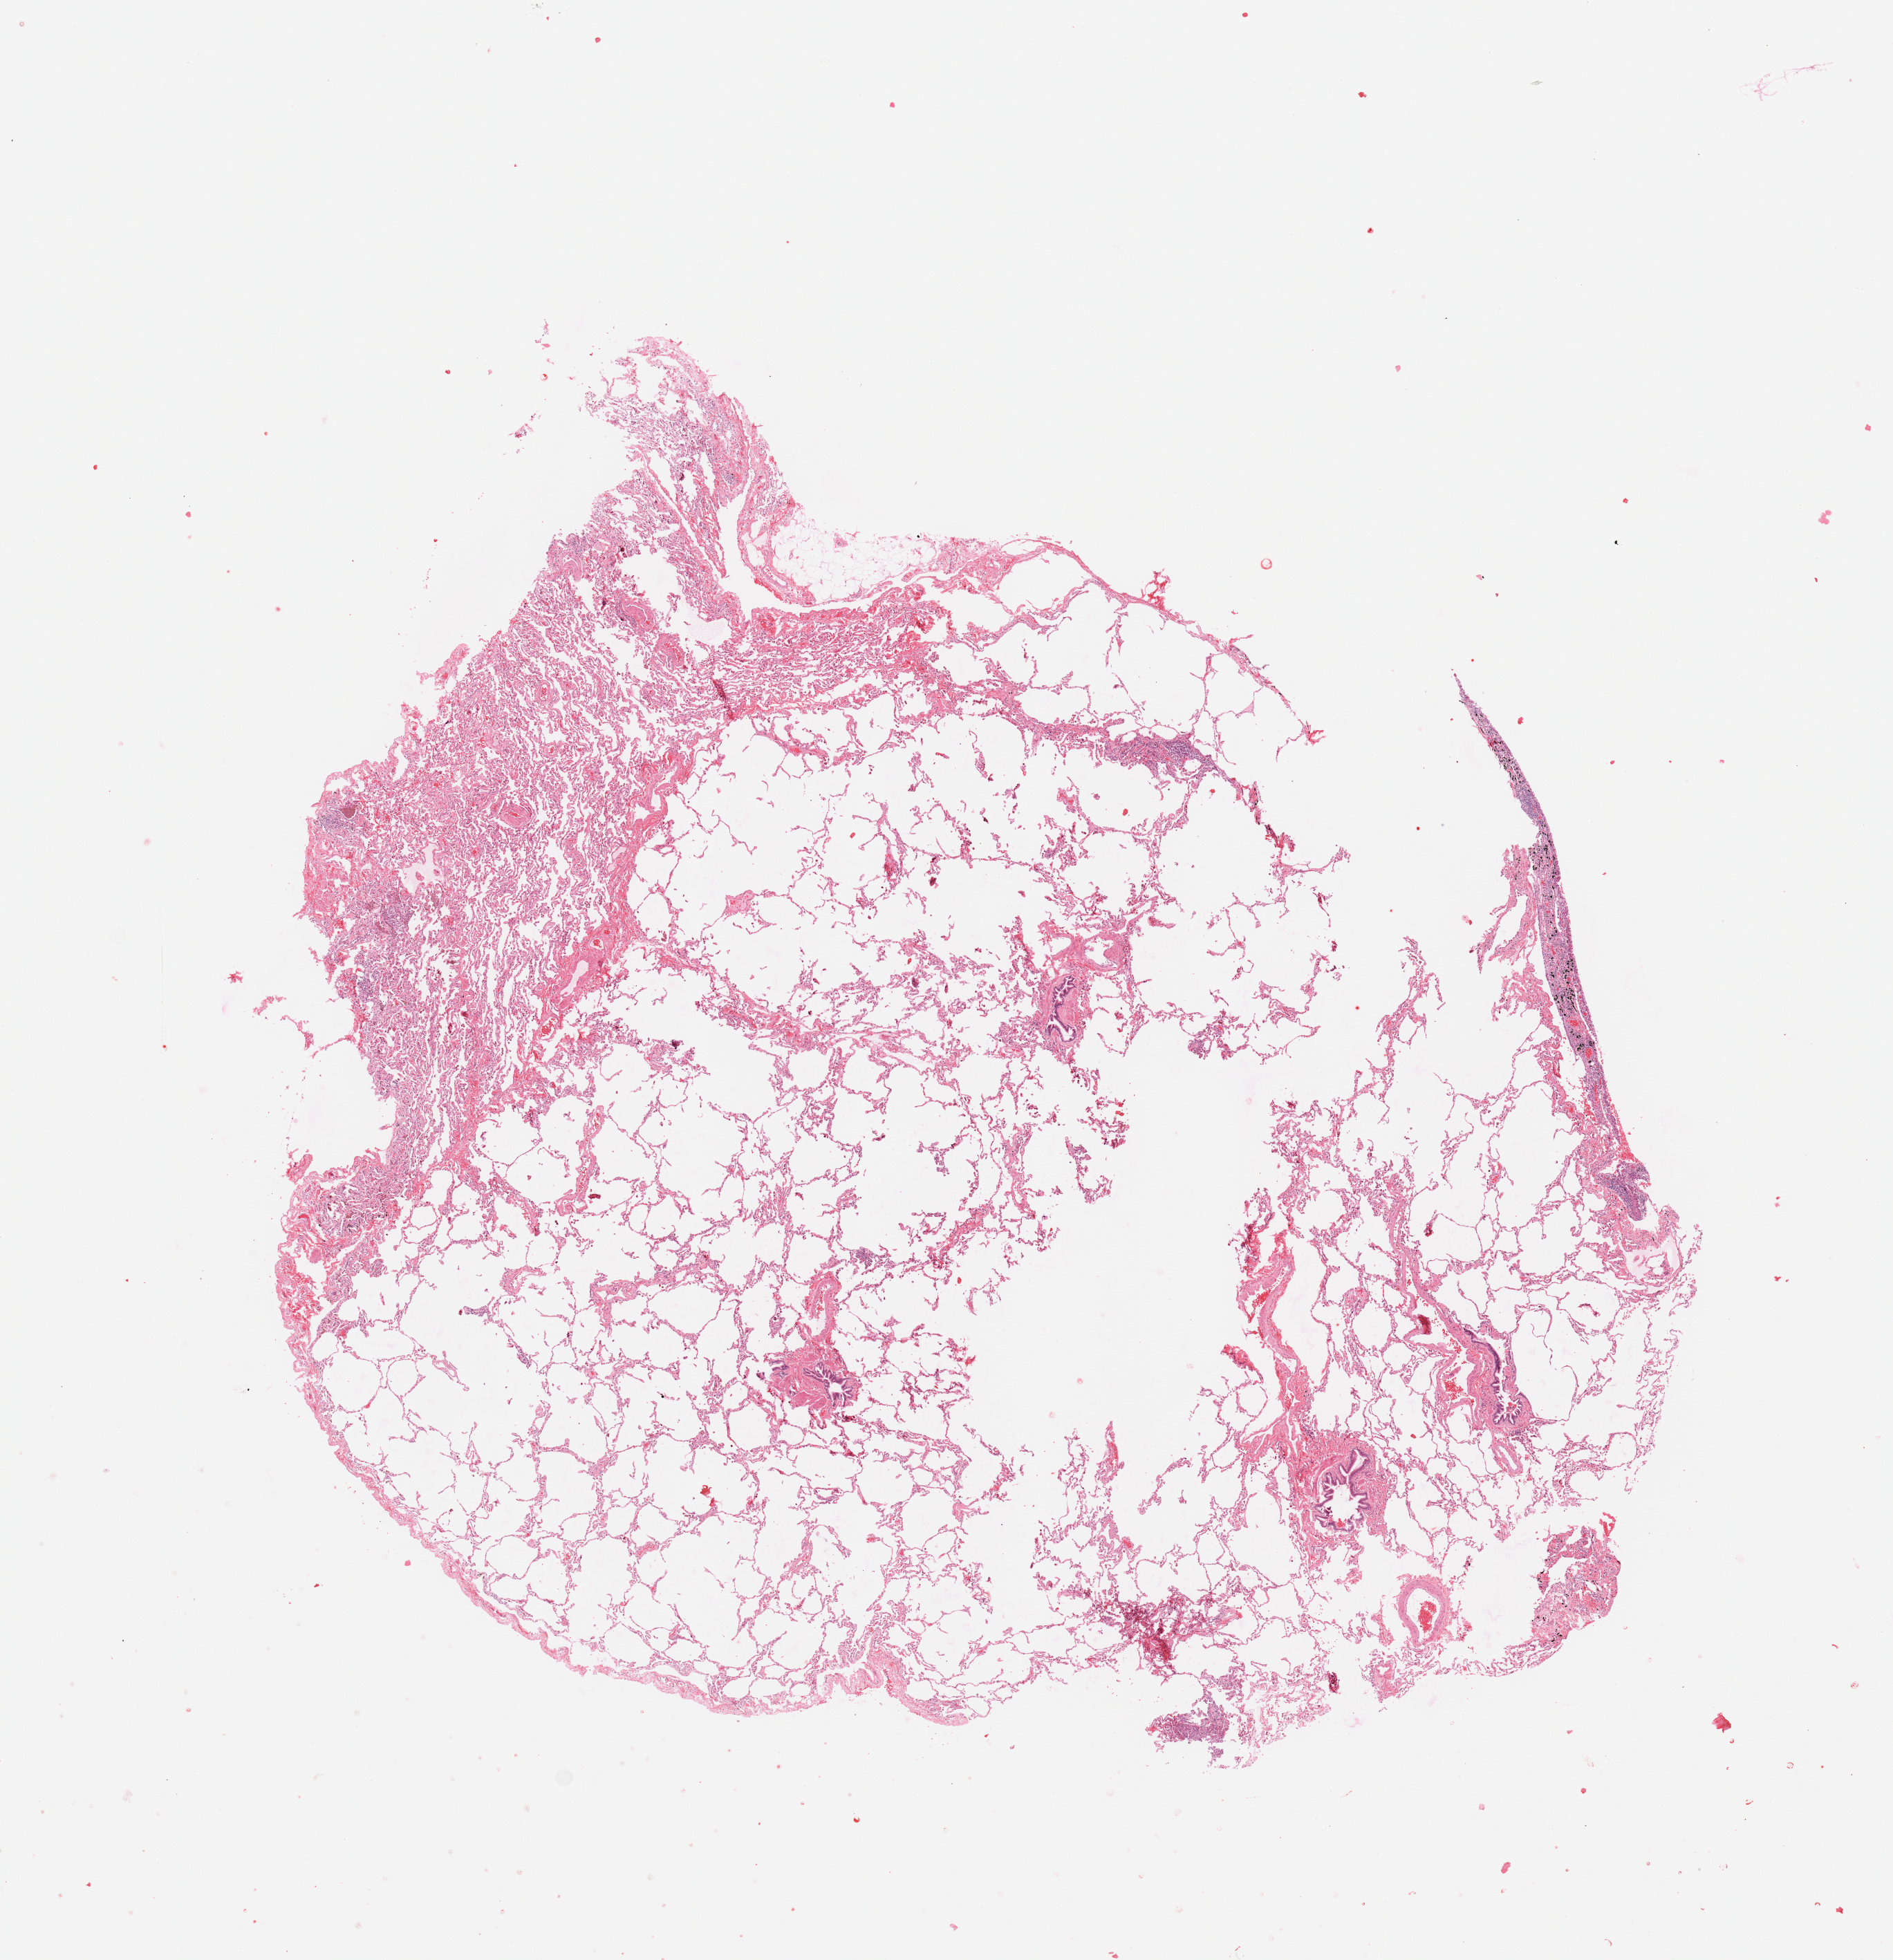
H&E whole-slide image, low-resolution overview of the scanned area, about 10.8 x 11.2 mm (acquisition: 20x scan). Normal (non-tumour) tissue sample, sampled site: lung. Male, 51 y/o.
This section: normal (non-tumour) tissue from the same patient. Patient diagnosis: Adenocarcinoma, NOS.